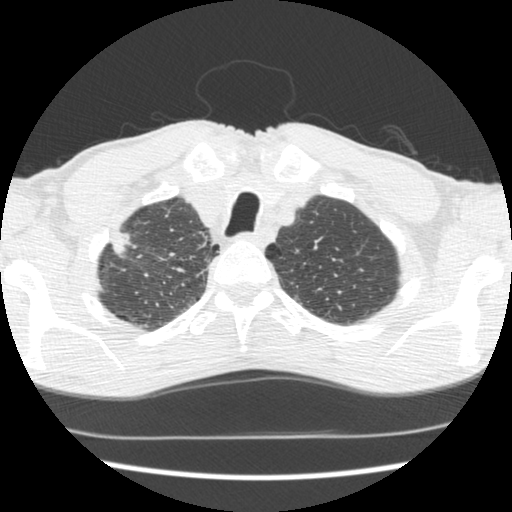
Low-dose screening chest CT, axial slice; first (baseline) screen; lung window (W 1500 / L -600 HU); 2.5 mm slice thickness; standard (soft-tissue) reconstruction kernel (STANDARD); slice 32 of 197 in the series. Male participant, aged 62 years at enrolment. Current smoker at enrolment.
• Expert reader's lesion annotation, bounding box [x1, y1, x2, y2] px = [94, 224, 145, 274].
• No non-calcified nodule or mass ≥4 mm was recorded by the screening reader at this exam.
• Official screen result: negative screen, significant abnormalities not suspicious for lung cancer.
• Participant outcome: lung cancer diagnosed 640 days after this screen (after the second annual screen) — adenocarcinoma, NOS, right upper lobe, poorly differentiated (G3), stage IIA (AJCC 6th edition), 22 mm at pathology.